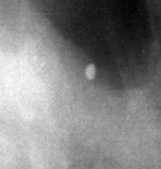
Cropped region of a digitized screen-film mammogram centred on a radiologist-marked abnormality; left breast; CC view.
Marked abnormality: calcifications, morphology lucent center / punctate; BI-RADS assessment category 2; benign without callback (not worked up further).